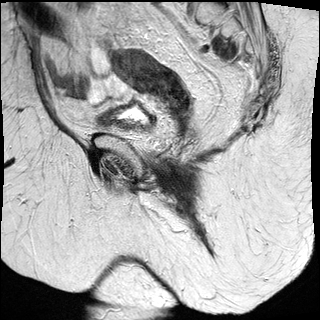
Pelvic MRI for cervical cancer, one sagittal slice; position 11 of 27 along the scan axis; T2-weighted; 1.5 T; TE 89 ms, TR 2740 ms; 4 mm slice thickness; 320 × 320 image matrix, field of view 260 × 260 mm. Female patient, age 67 years.
Structures marked on this image (expert manual segmentation):
- uterus and cervix: box from (x=111, y=48) to (x=194, y=121) px